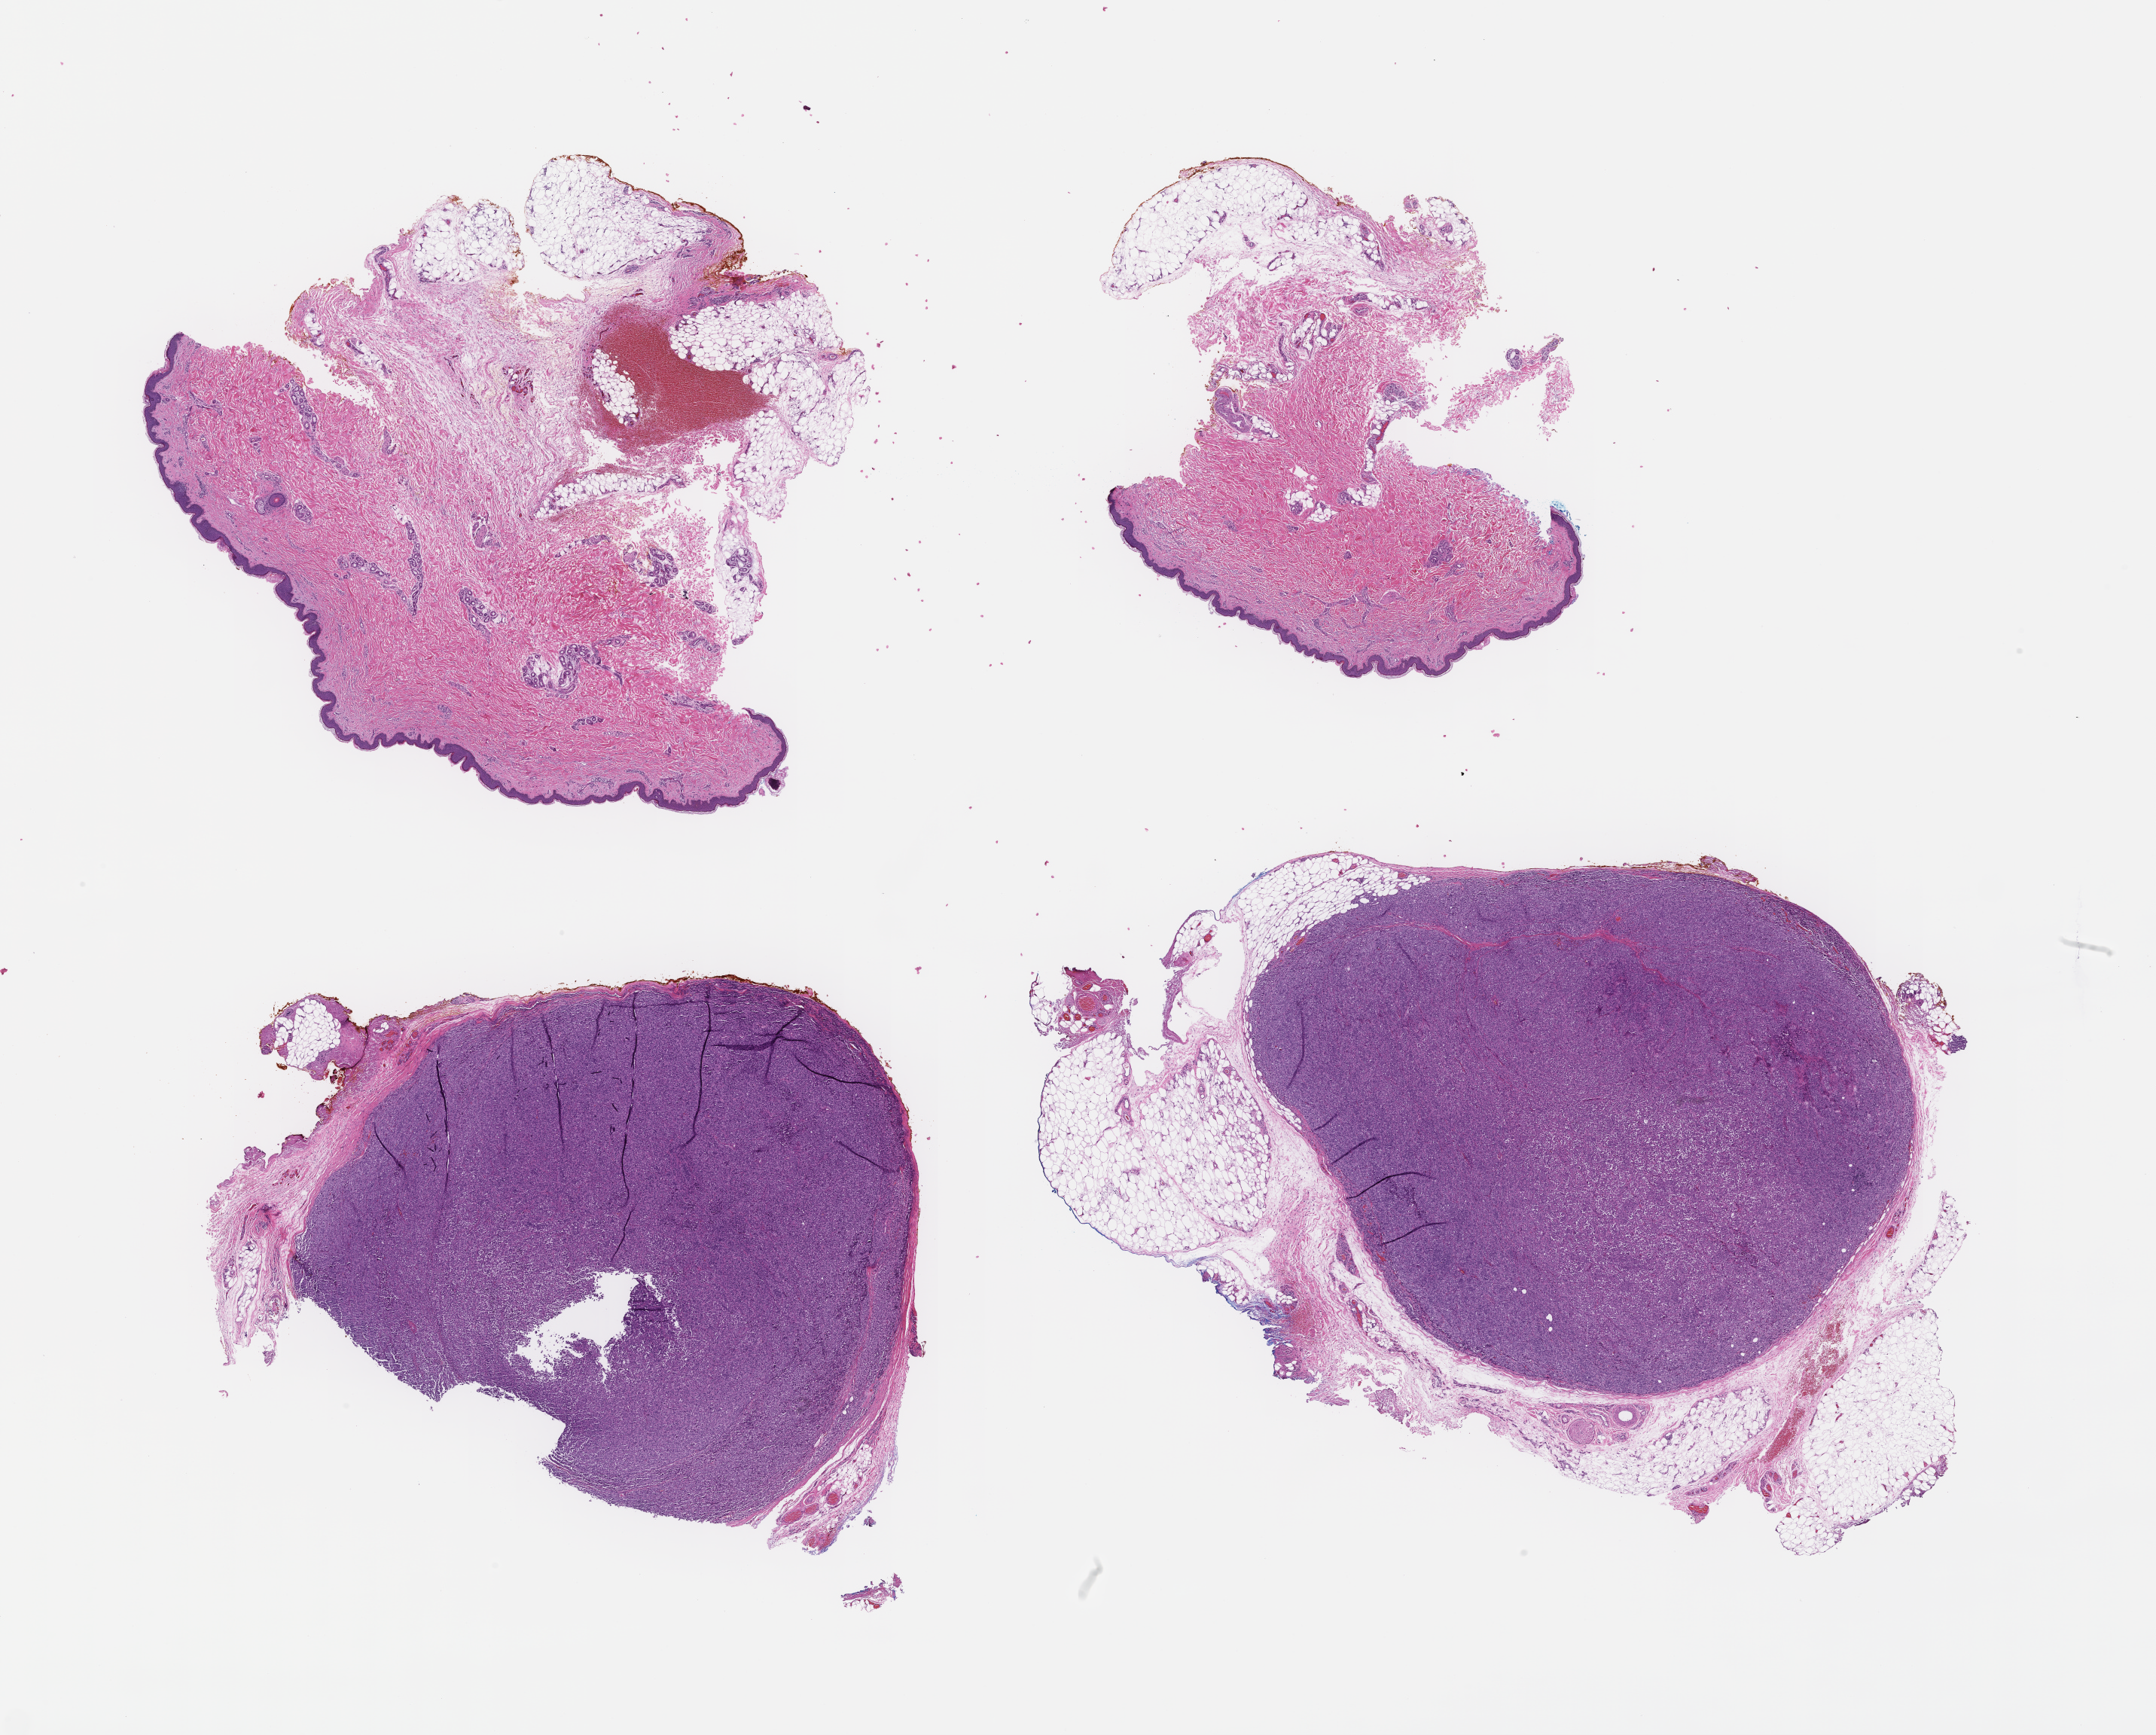
Digitized hematoxylin and eosin (H&E)-stained section, a low-resolution overview of the entire scanned area, about 23.1 x 18.6 mm. FFPE section. Specimen time point: archival tissue. Patient: male.
- this section: metastatic tumor tissue
- patient diagnosis (primary): Melanoma